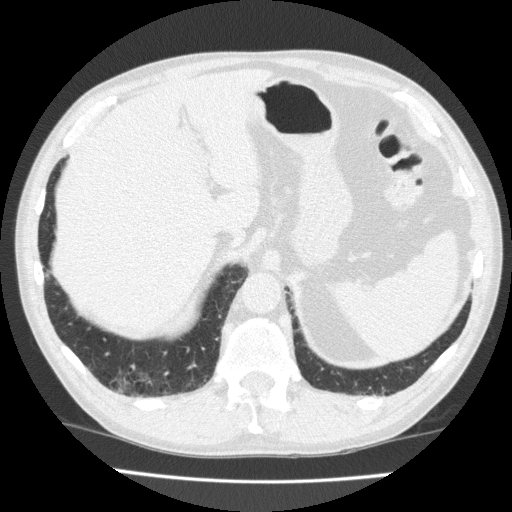
Chest CT (low-dose screening protocol), one axial image; first (baseline) screen; lung window (W 1500 / L -600 HU); standard (soft-tissue) reconstruction kernel (FC10); slice 185 of 226 in the series. Male, age 70 years at enrolment. Current smoker at enrolment.
Expert reader's lesion annotation, box from (x=112, y=360) to (x=161, y=399) px. Screening reader's record for this exam: no non-calcified nodule ≥4 mm recorded. Official screen result: negative screen, significant abnormalities not suspicious for lung cancer. Participant outcome: lung cancer diagnosed 503 days after this screen (after the second annual screen) — squamous cell carcinoma, NOS, right lower lobe, moderately differentiated (G2), stage IA (AJCC 6th edition), 20 mm at pathology.